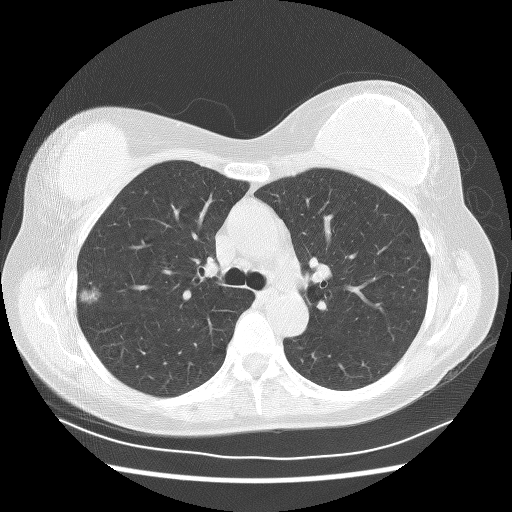
Chest CT (low-dose screening protocol), one axial image. Baseline annual screen. Lung window (W 1500 / L -600 HU). 2.5 mm slice thickness. Lung (sharp) reconstruction kernel (BONE). Slice 80 of 253 in the series. 512 × 512 image matrix, field of view 340 × 340 mm. Female, age 58 years at enrolment.
Expert reader's lesion annotation, bounding box [x1, y1, x2, y2] px = [65, 272, 112, 312]. The screening reader recorded 2 non-calcified nodules or masses ≥4 mm on this exam; which of them this box marks is not recorded.